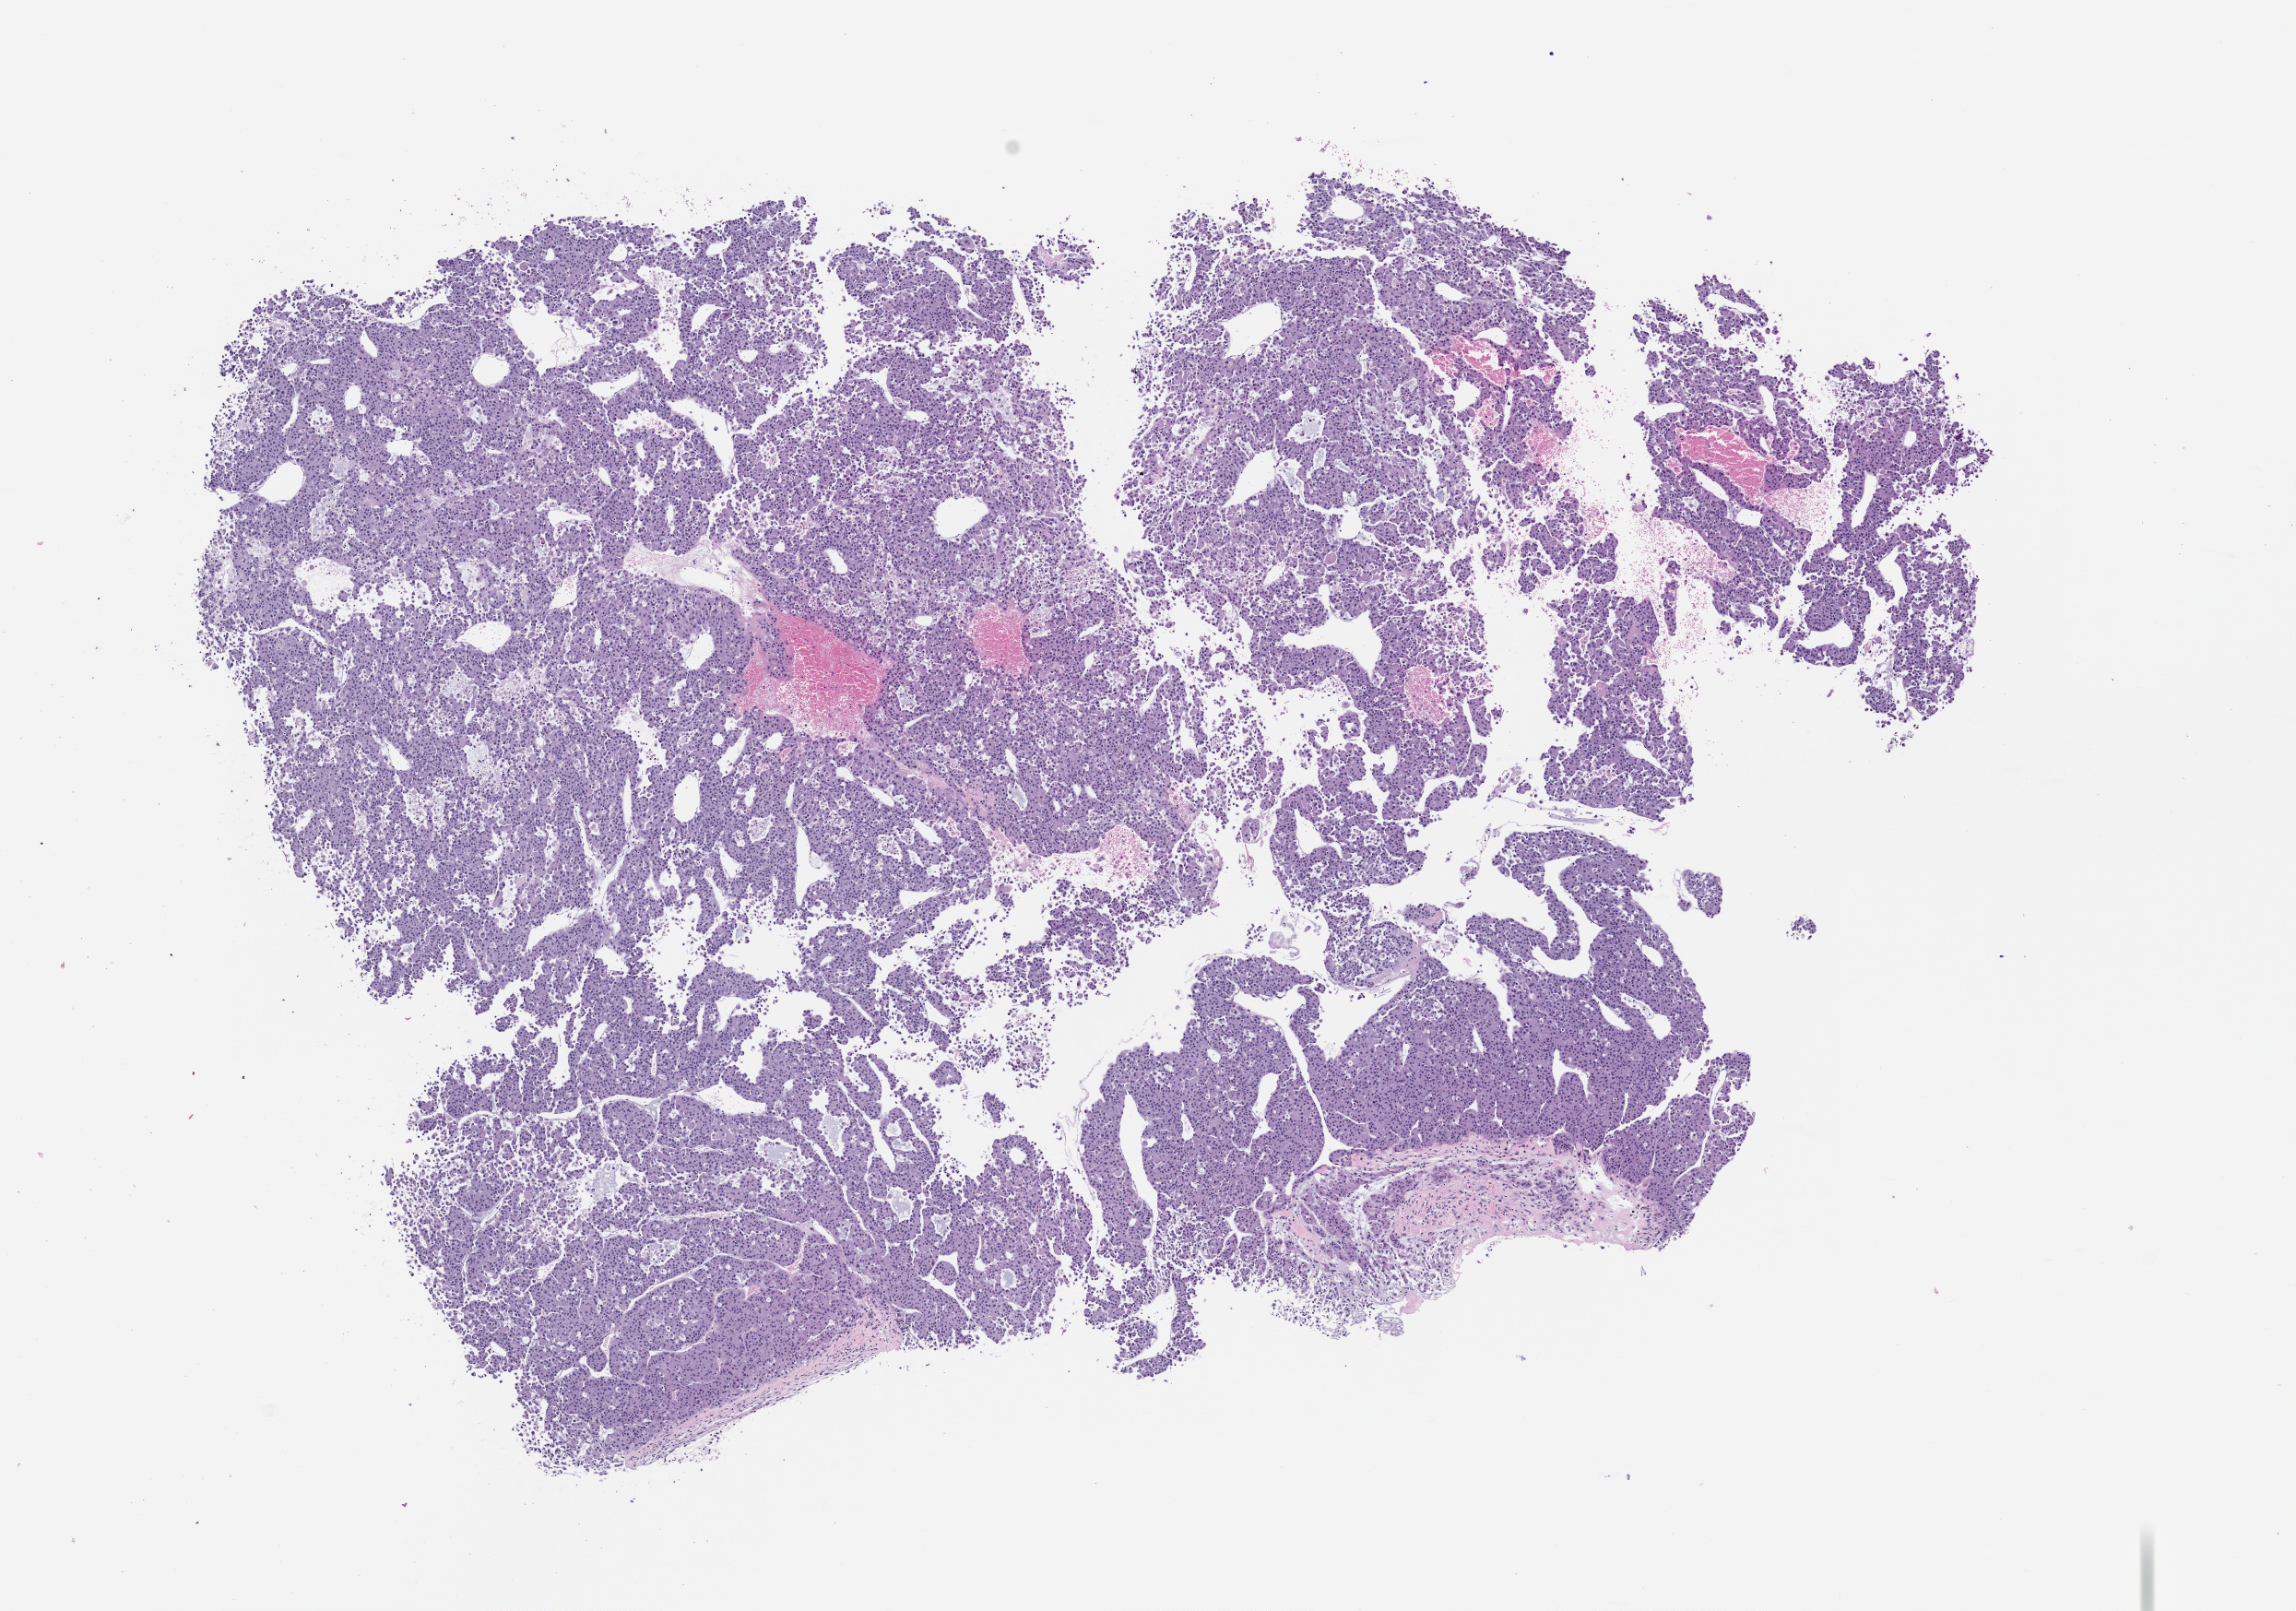
Whole-slide image, haematoxylin and eosin: patient-derived xenograft (human tumor grown in a mouse) — whole scanned area (about 10.0 x 7.0 mm) shown as a low-resolution overview; formalin-fixed paraffin-embedded section; tumor site category: adrenal cortex.
Originating patient diagnosis: Adrenal Cortical Carcinoma.